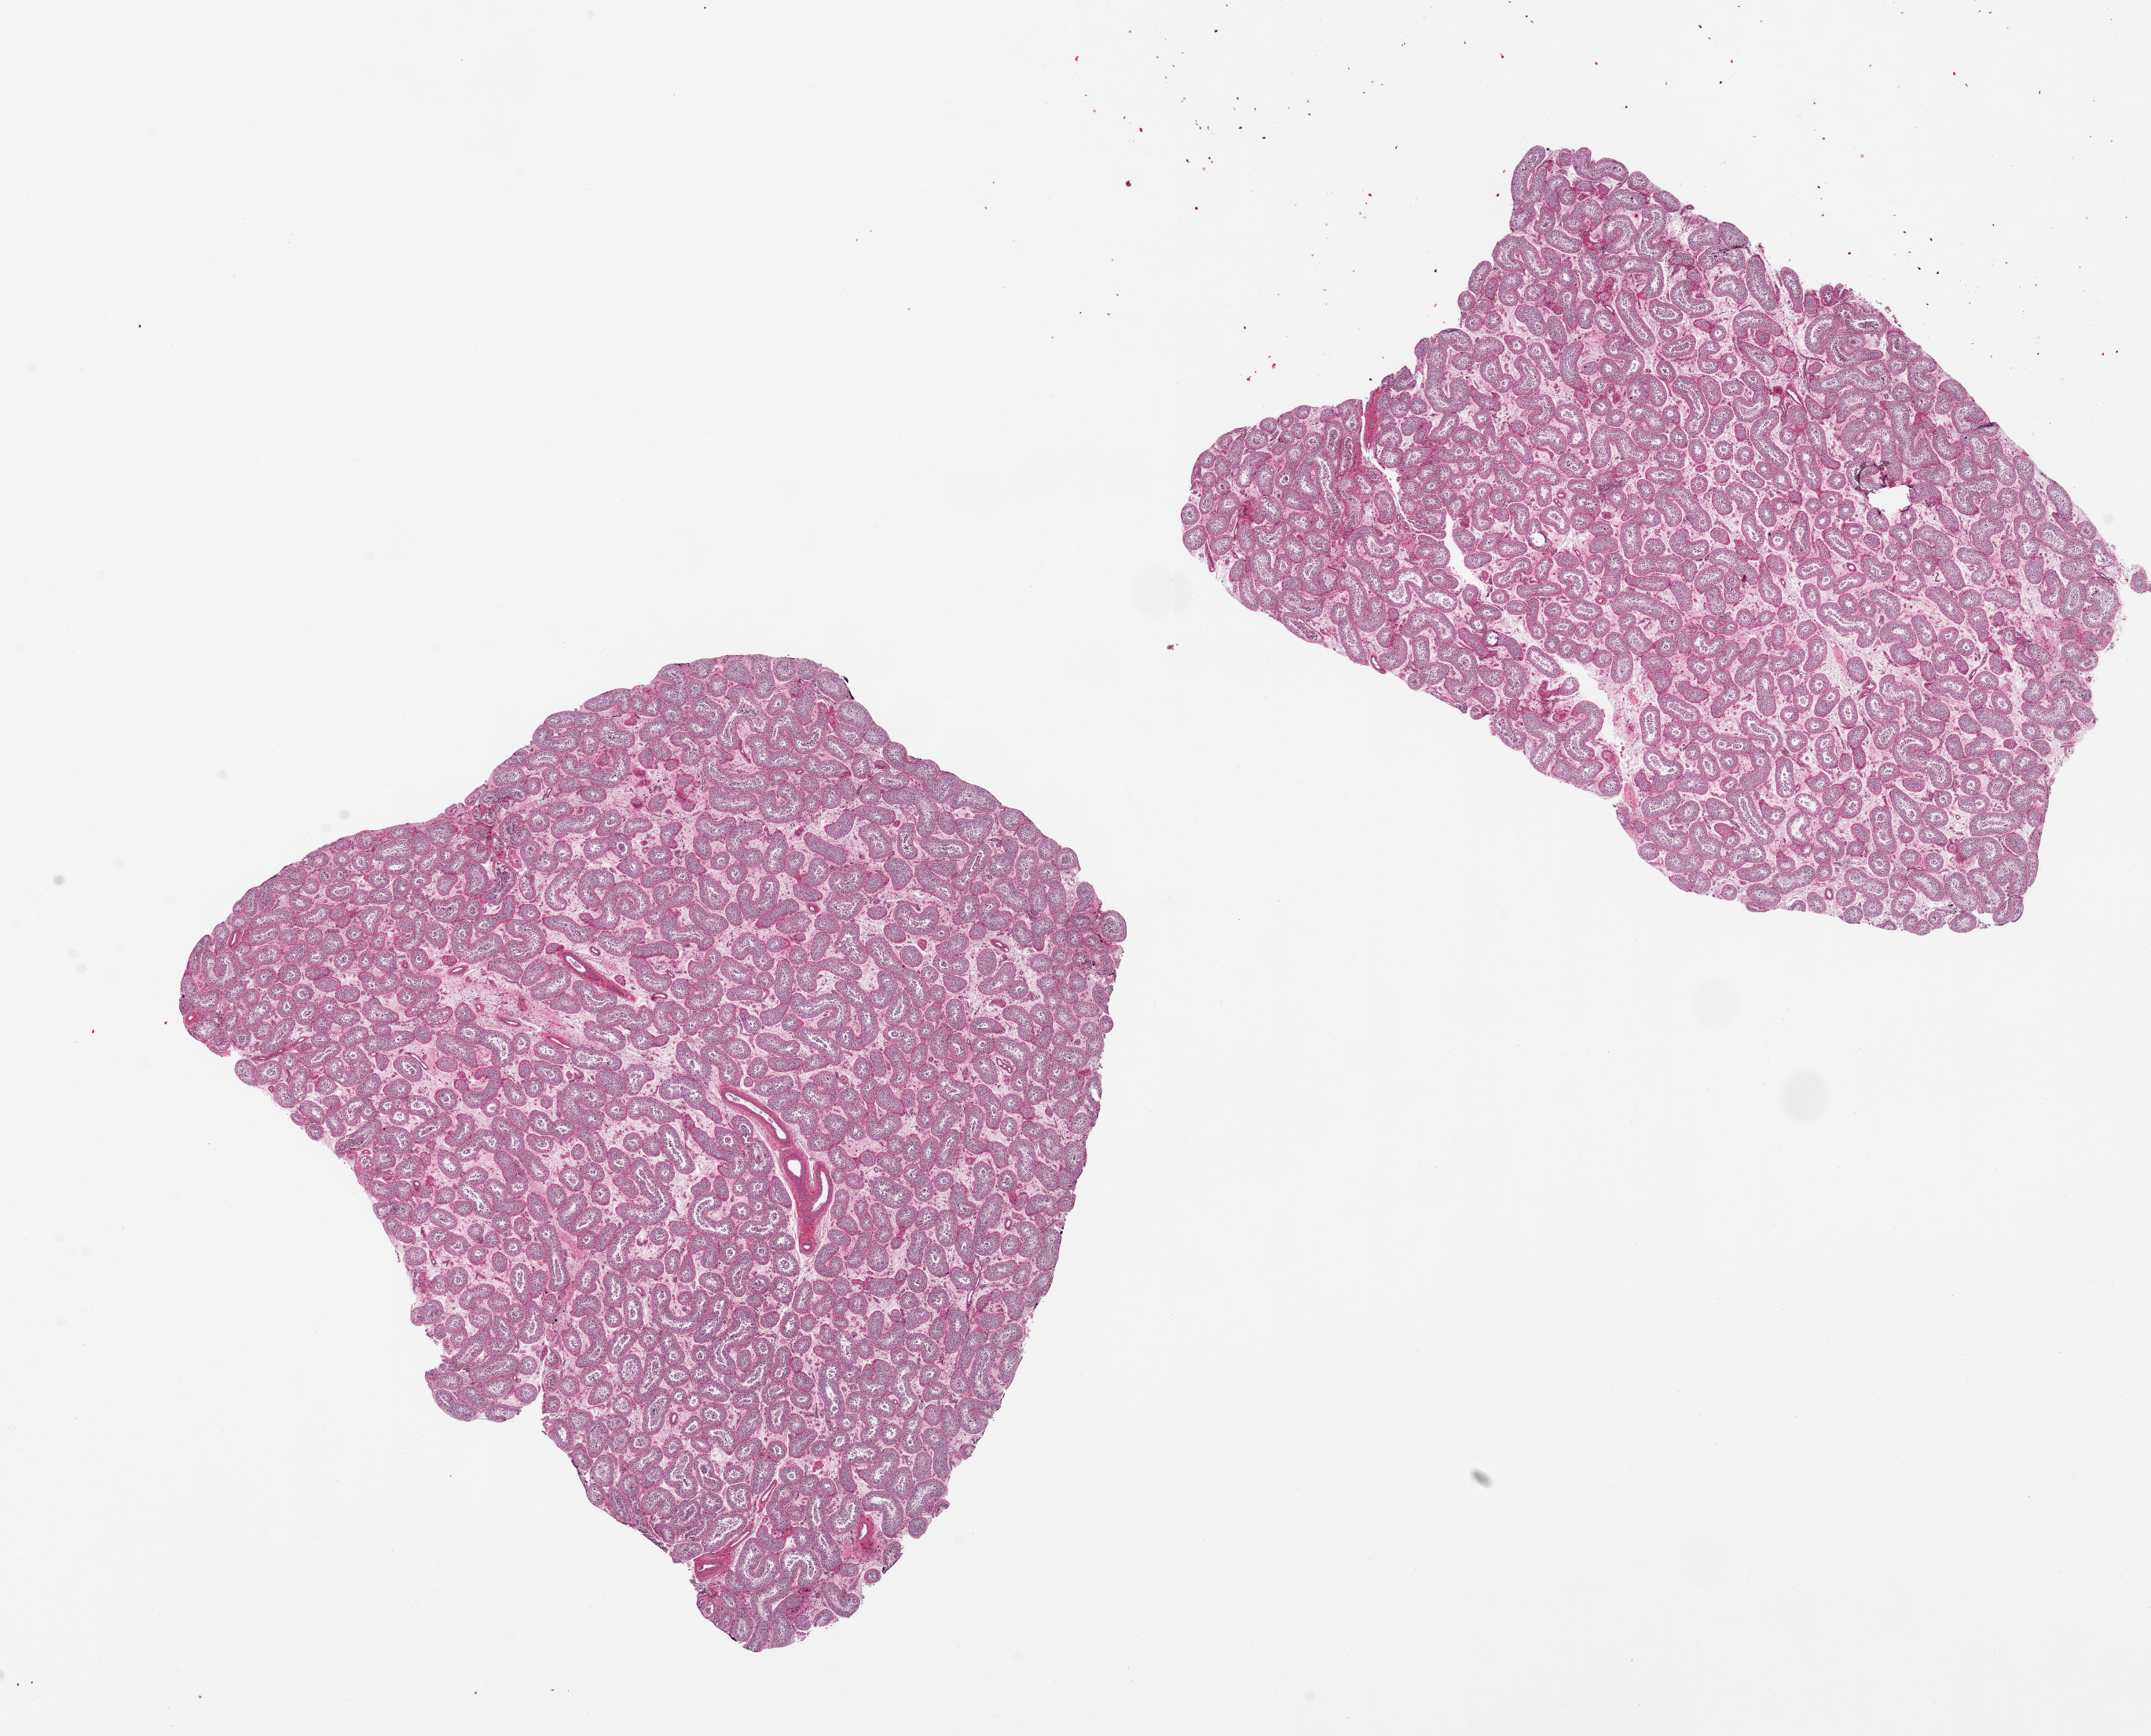
Digitized haematoxylin and eosin-stained section, brightfield, low-resolution overview of the scanned area, about 21.7 x 17.5 mm (acquisition: 20x scan). PAXgene-fixed paraffin-embedded (PFPE) section. Sampled site (target tissue): testis. Tissue donor sample.
Pathologist's review note for this sample: 2 pieces. 9.5x8 & 10x6mm; Active spermatogenesis.